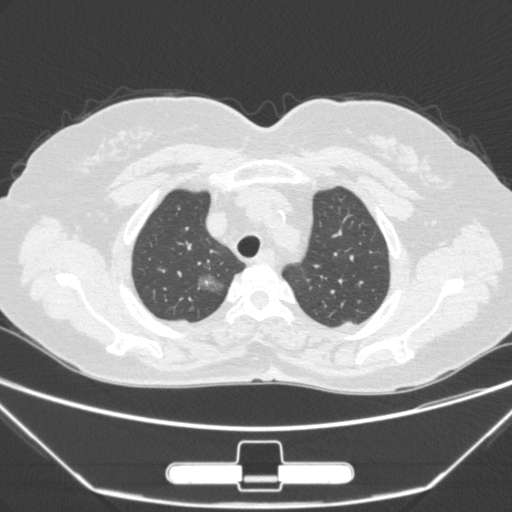
Chest CT, one axial slice. Position 229 of 275 along the scan axis. 120 kVp. Lung window (W 1500 / L -600 HU). 512 × 512 image matrix, field of view 356 × 356 mm. Female patient, age 63 years. From the clinical record (not read from this slice): clinical TNM (as recorded): T1a N0 M0.
Outlined on this slice (rectangle marked by the reading radiologist):
- lung tumour (recorded histology: adenocarcinoma): bounding box <188,264,225,309> (left, top, right, bottom; pixels)